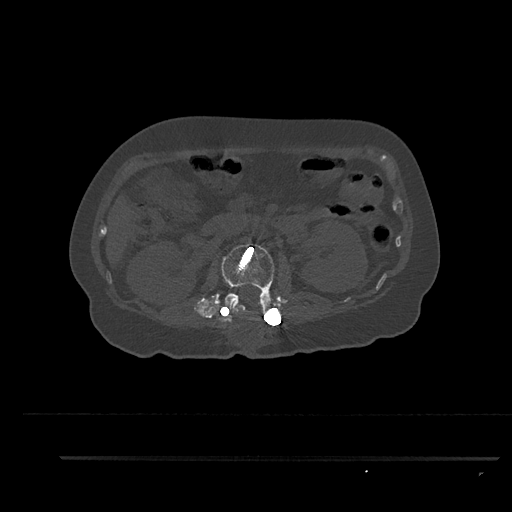
CT including the spine, one axial slice; position 178 of 797 along the scan axis; 120 kVp; bone window (W 1800 / L 400 HU); 0.5 mm slice thickness; 512 × 512 image matrix. Female patient, age 44 years. From the clinical record (not read from this slice): primary cancer: renal; vertebrae with lytic lesions (as recorded): L1.
Outlined on this slice (semi-automatically segmented with operator editing):
- L2 vertebra: bounding box <216,242,275,322> (left, top, right, bottom; pixels)